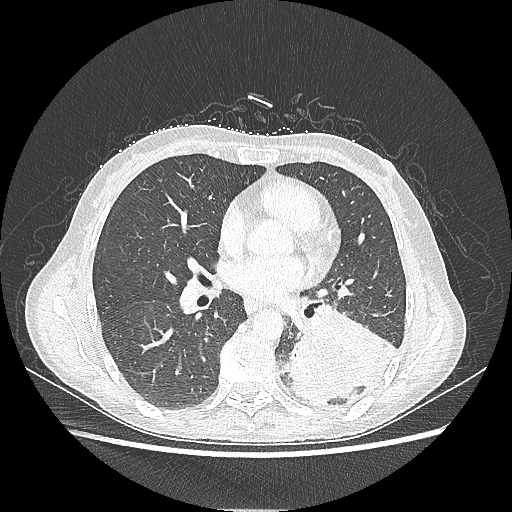
Chest CT, one axial slice. Position 110 of 220 along the scan axis. Lung window (W 1500 / L -600 HU). 1.25 mm slice thickness. 512 × 512 image matrix, field of view 360 × 360 mm. Patient: female, 53 years. Case-level facts recorded for this patient, not image findings: clinical TNM (as recorded): T3 N0 M0.
Outlined on this slice (rectangle marked by the reading radiologist):
- lung tumour (recorded histology: adenocarcinoma): box from (x=288, y=304) to (x=400, y=404) px